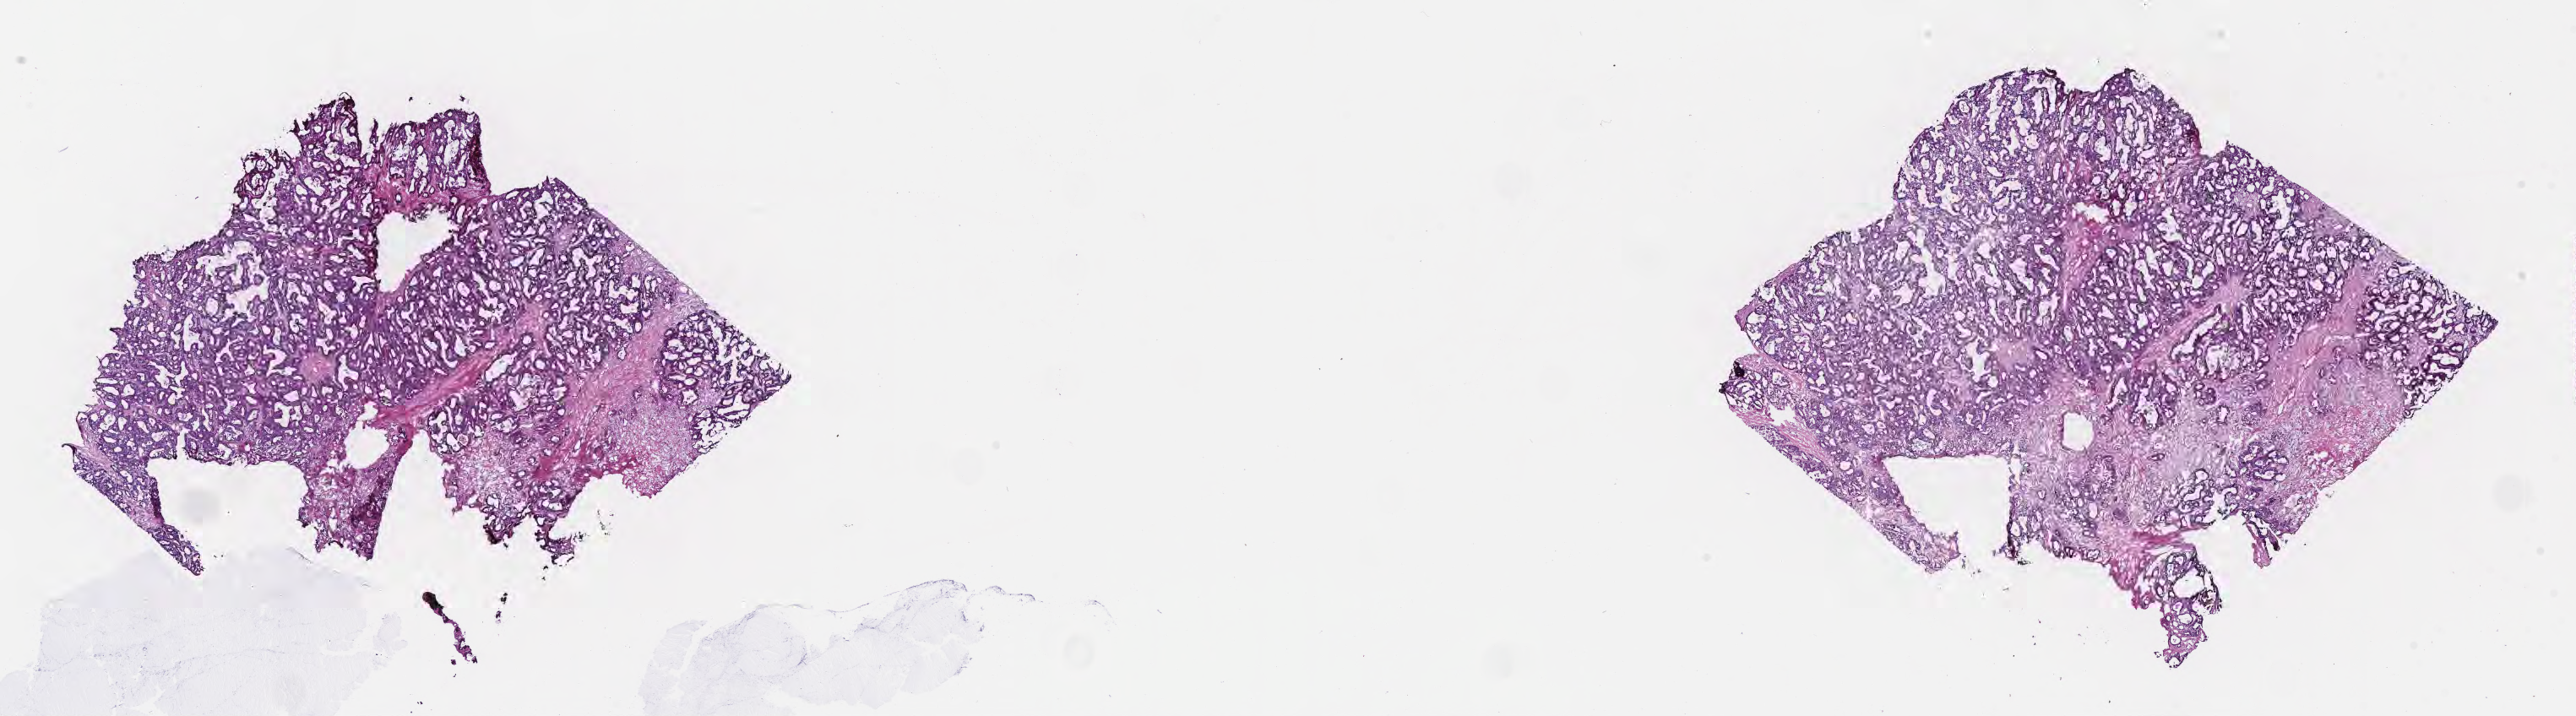
Whole-slide image, haematoxylin and eosin stain, whole scanned area (about 24.7 x 6.9 mm) shown as a low-resolution overview, cryosection, specimen: metastatic tumor tissue, resected from liver. Male patient; age at initial diagnosis 61 years. Slide review estimates, as recorded: tumor cells 85%, tumor nuclei 85%, stromal cells 15%, necrosis 0%, normal cells 0%. Inflammatory infiltration, as recorded: lymphocyte infiltration 5%, monocyte infiltration 2%, neutrophil infiltration 4%.
* patient diagnosis (primary): Adenocarcinoma, metastatic, NOS